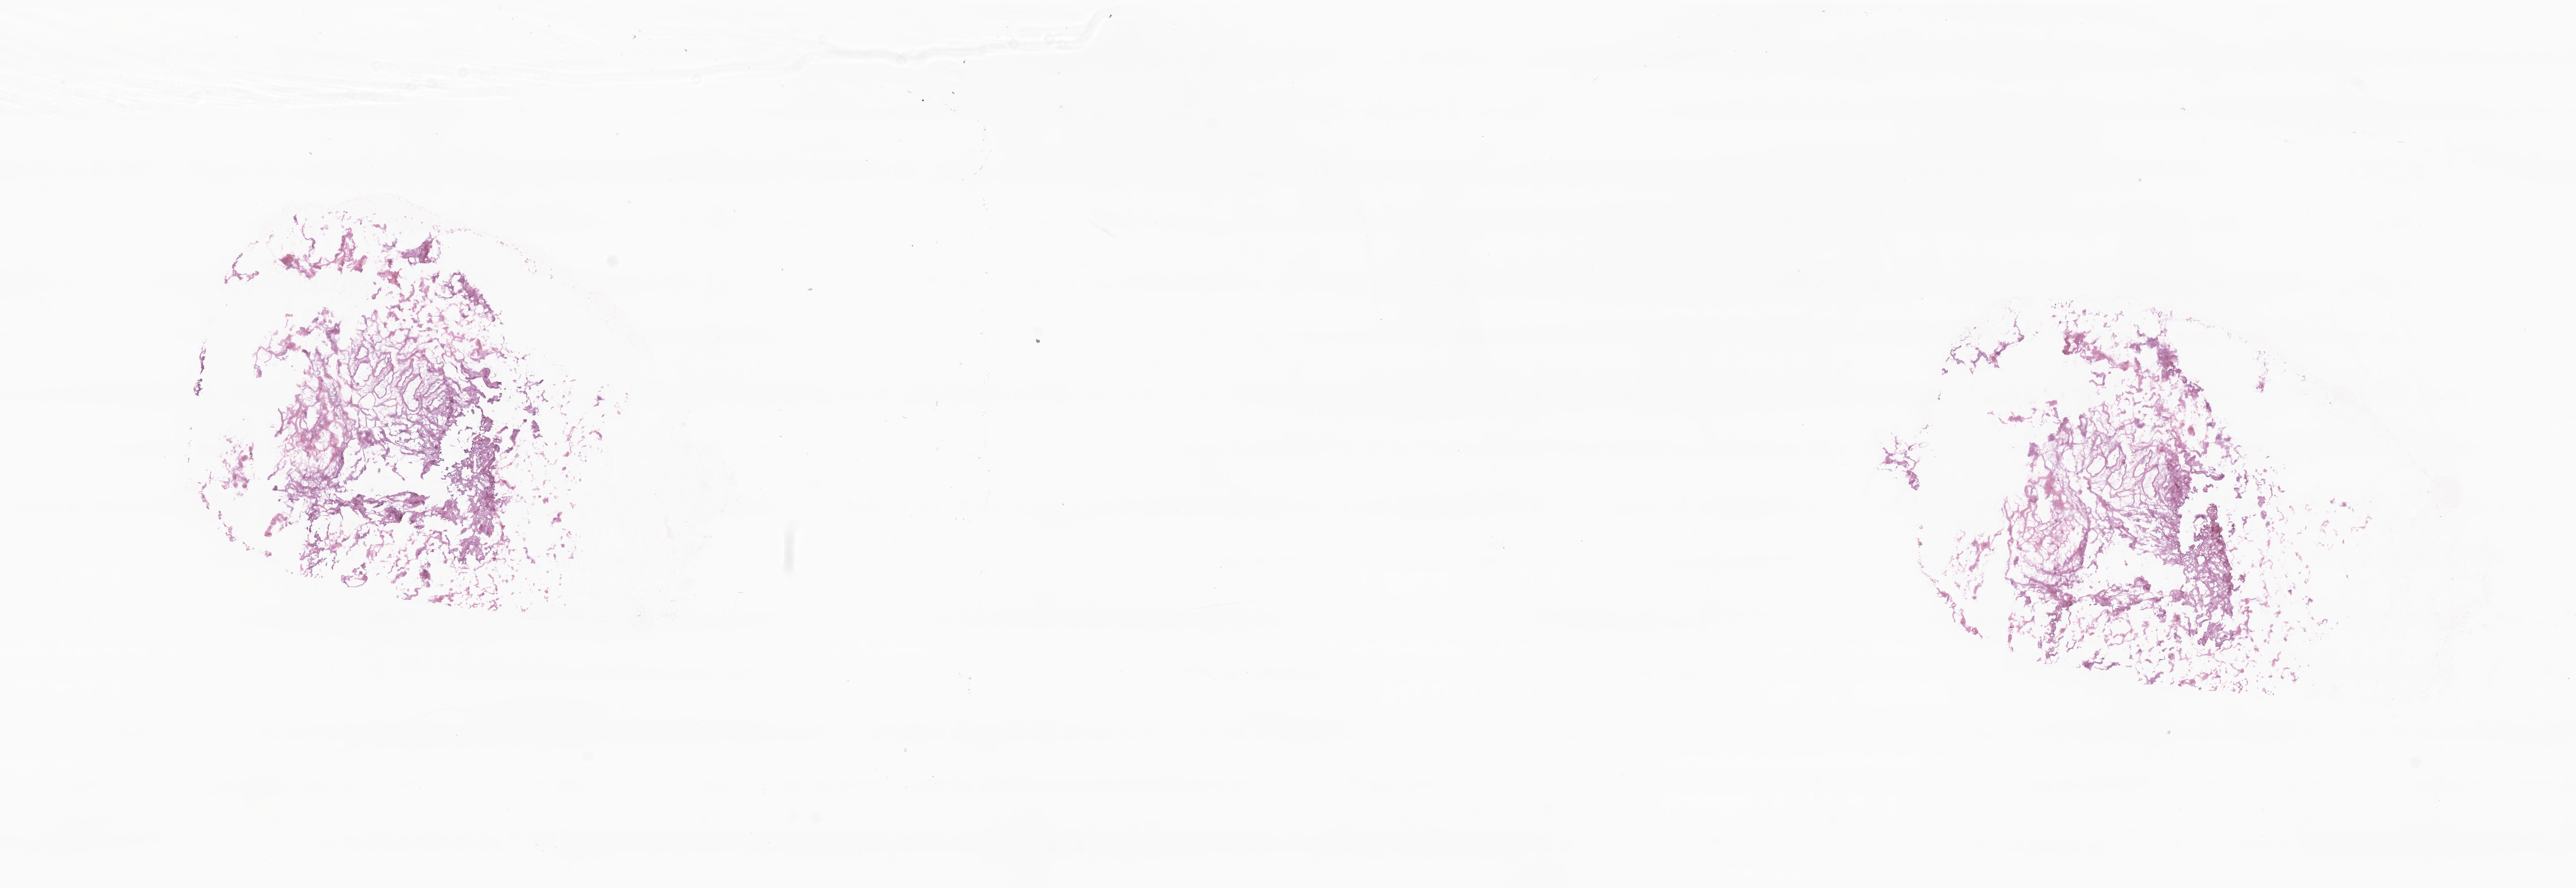
Digitized haematoxylin and eosin-stained section, a low-resolution overview of the entire scanned area, about 24.5 x 8.5 mm, frozen section, specimen: normal-tissue sample (non-tumor) from a patient with leiomyosarcoma, NOS. Patient: female, age at initial diagnosis 60 years. Pathologist review of this section (percent, as recorded): tumor cells 0%, tumor nuclei 0%, stromal cells 0%, necrosis 0%, normal cells 100%. Inflammatory infiltration, as recorded: lymphocyte infiltration 0%, monocyte infiltration 0%, neutrophil infiltration 0%.
• this section: non-tumor tissue sample; the patient's diagnosis is given above
• section: bottom of the tissue portion